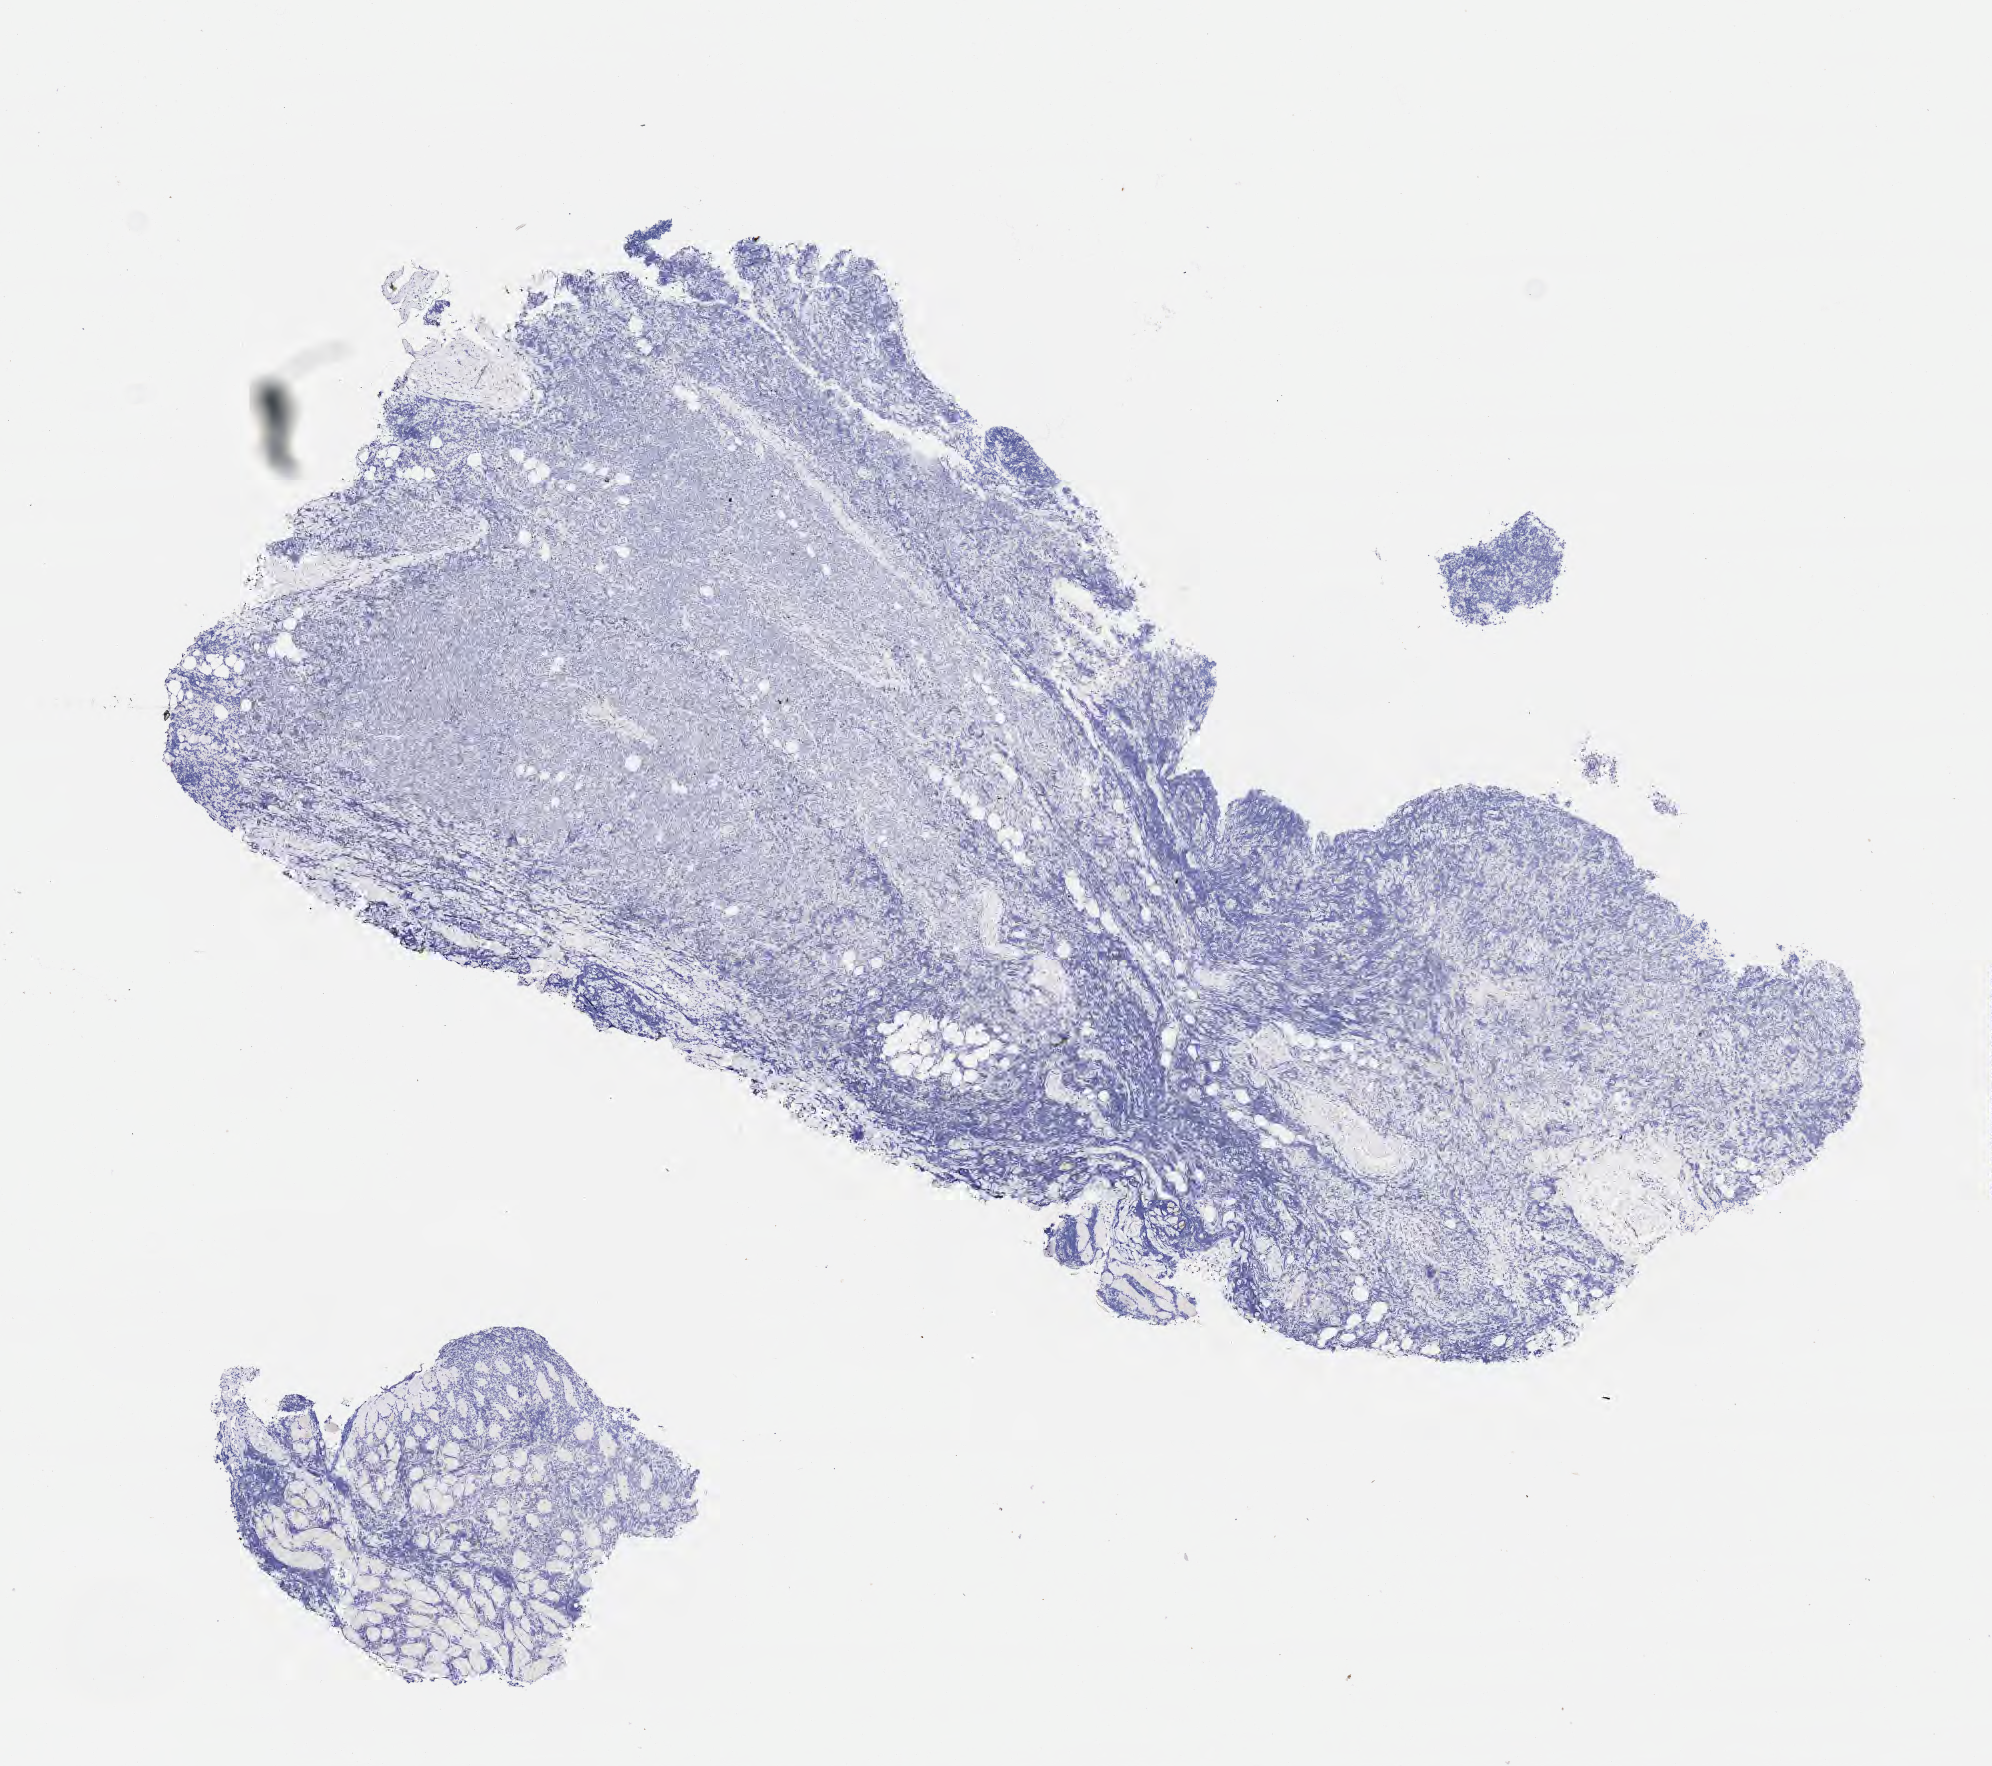
Whole-slide image, immunohistochemical stain for p53 — low-resolution overview of the scanned area, about 8.0 x 7.1 mm; specimen: tumor tissue. Patient: male, 67 years old.
Diagnosis: Diffuse large B-cell lymphoma, NOS.